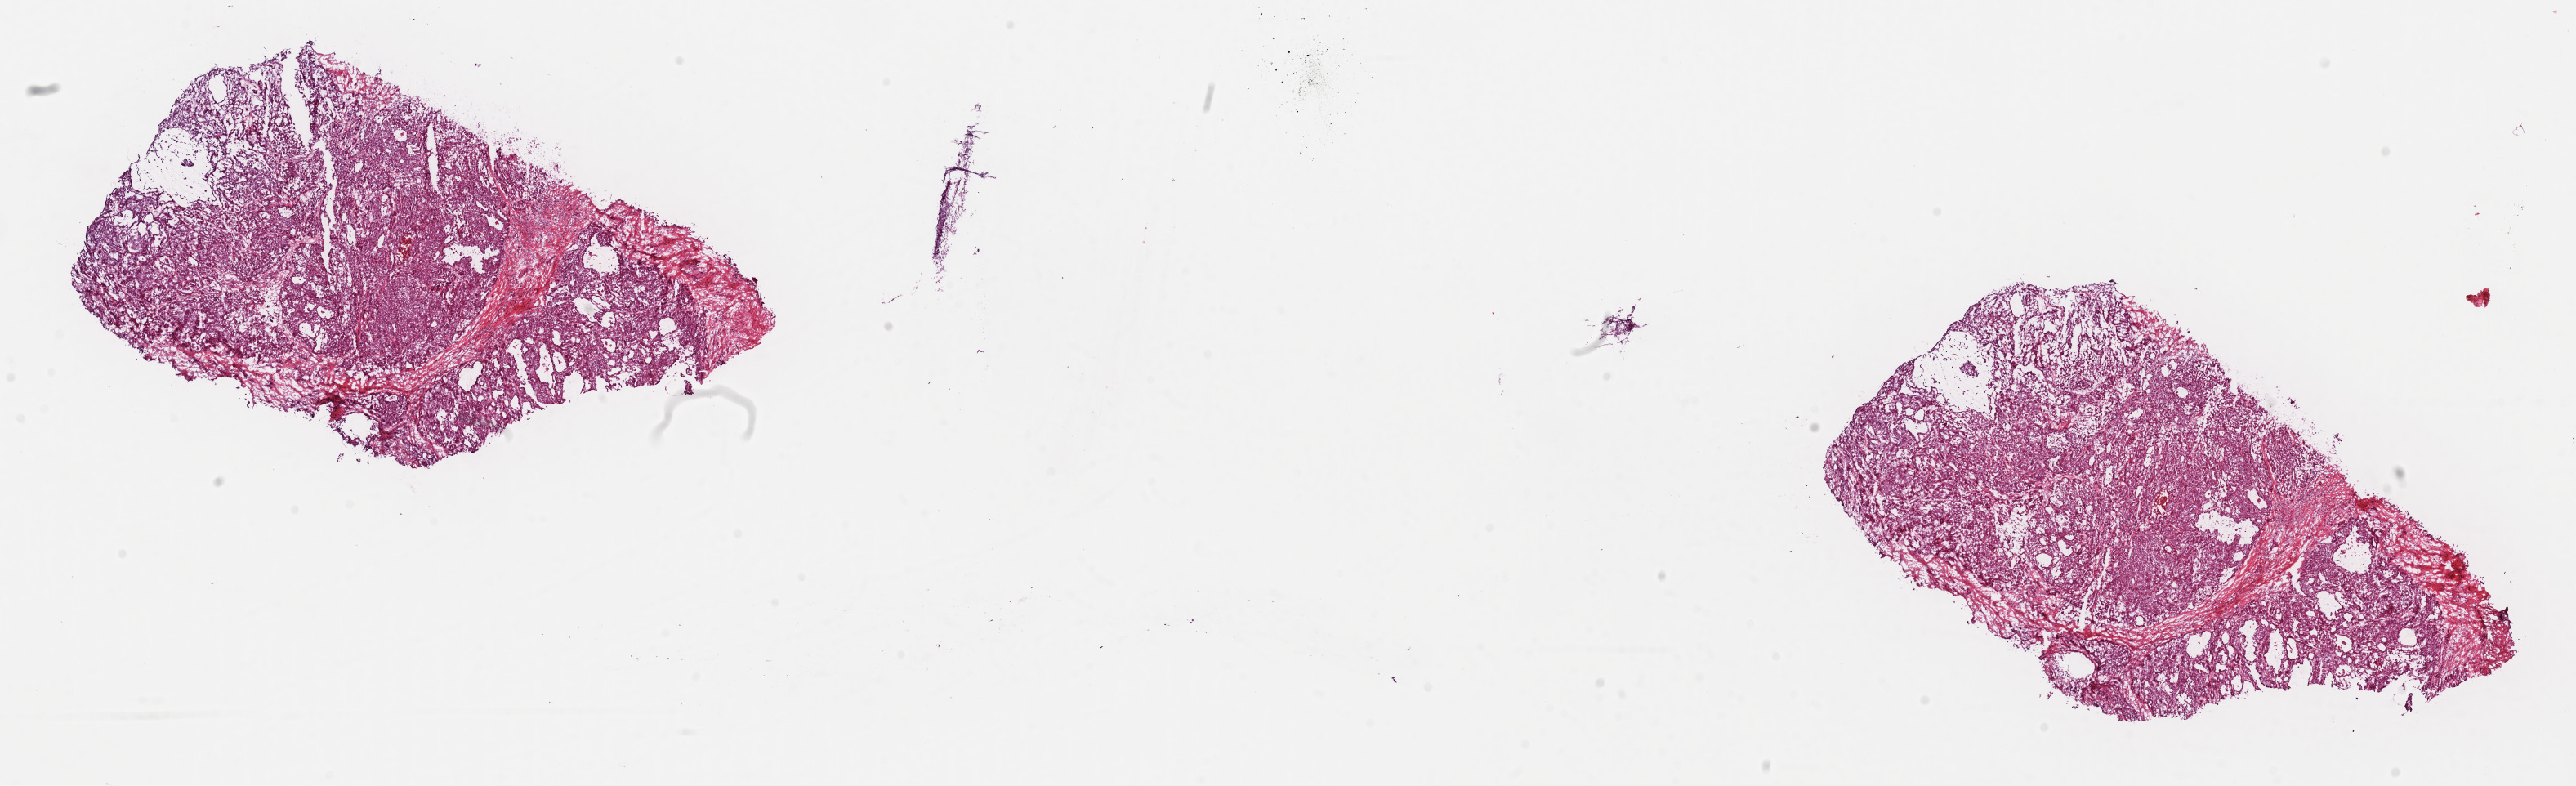
Whole-slide histology image, Hematoxylin and eosin (H&E) stained, a low-resolution overview of the entire scanned area, about 24.9 x 7.6 mm (acquisition: 40x scan). Frozen section from the top of the tissue portion. Primary tumour sample from the thyroid. Female patient; age at initial diagnosis 37 years. Slide review estimates, as recorded: tumour cells 85%, tumour nuclei 85%, normal cells 0%, stromal cells 15%, necrosis 0%. Inflammatory infiltration, as recorded: lymphocyte infiltration 2%, monocyte infiltration 0%, neutrophil infiltration 0%.
AJCC pathologic stage: I (7th edition). Diagnosis: Papillary carcinoma, follicular variant (thyroid gland). TNM: T1b NX MX. Laterality: right.